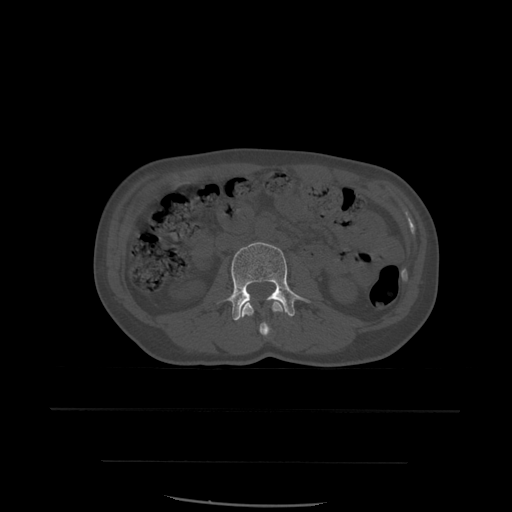
CT including the spine, one axial slice; slice 205 of 574 in the series (ordered by position); bone window (W 1800 / L 400 HU); 1.25 mm slice thickness; 512 × 512 image matrix, field of view 392 × 392 mm. Patient age 48 years. From the clinical record (not read from this slice): primary cancer: lung.
Outlined on this slice (semi-automatic segmentation, software-assisted and operator-edited):
- L2 vertebra: box from (x=241, y=301) to (x=284, y=337) px
- L3 vertebra: (x=227, y=242)–(x=310, y=321)